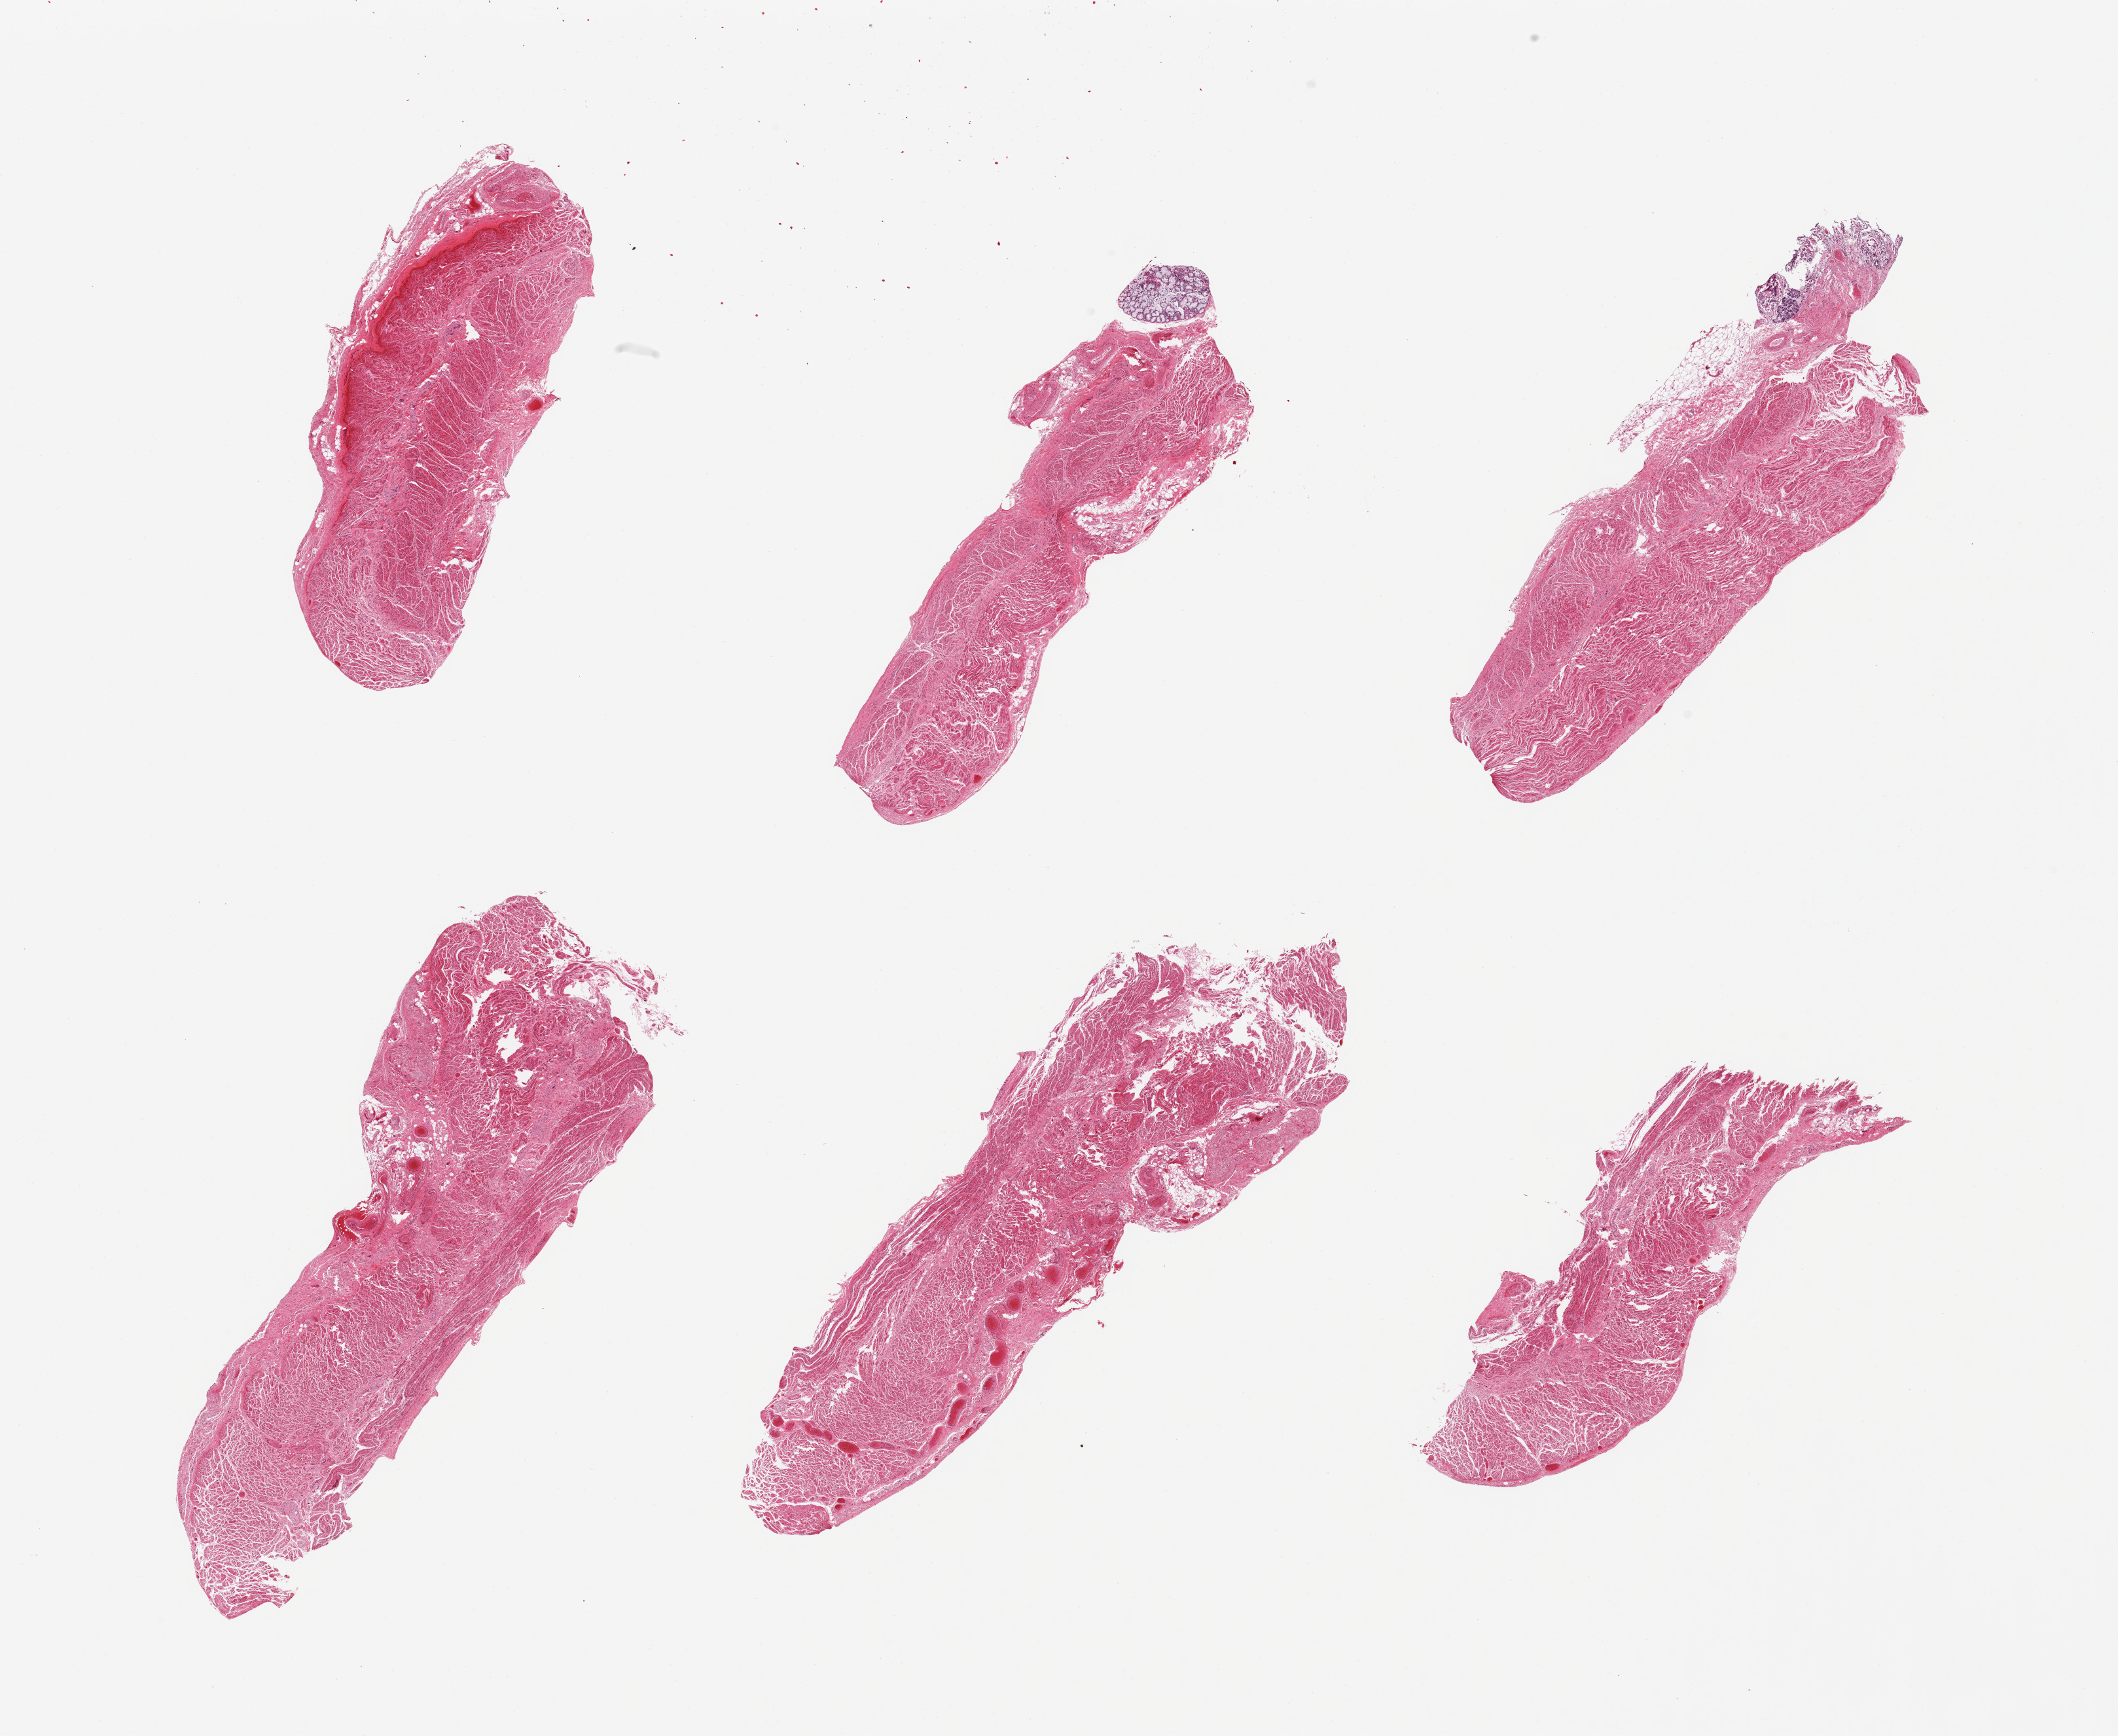
Digitized haematoxylin and eosin-stained section — shown as a low-resolution overview of the whole scanned area (about 25.6 x 21.0 mm, slide scanned at 20x), PAXgene-fixed, paraffin-embedded tissue, sampled site (target tissue): gastroesophageal junction, tissue donor sample. Female donor.
Pathologist's review note for this sample: 6 pieces, confirmed target muscularis, incidental ~1mm submucosal mucus gland.